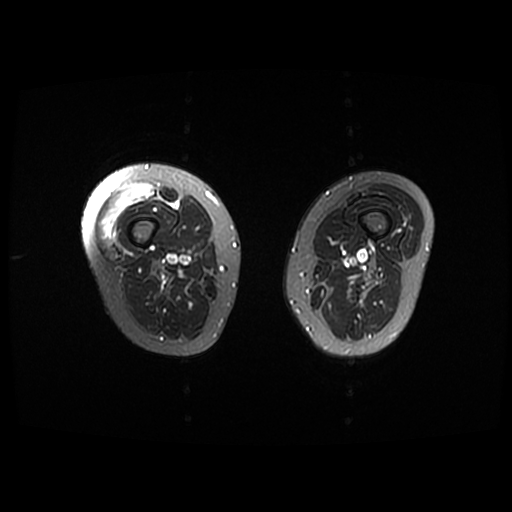
MRI of an extremity soft-tissue mass, one axial slice; slice 4 of 42 in the series (ordered by position); T2-weighted fat-saturated; 6 mm slice thickness; 512 × 512 image matrix, field of view 440 × 440 mm. Female patient. Case-level facts recorded for this patient, not image findings: histological type: pleiomorphic undifferentiated sarcoma; grade: high; site of the primary tumour: right quadricep.
Annotated regions visible in this slice (manually delineated by an expert):
- gross tumour volume including surrounding oedema: bounding box <98,183,157,240> (left, top, right, bottom; pixels)